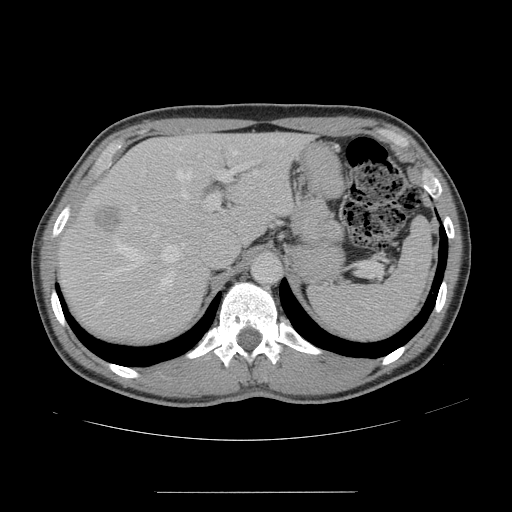
Contrast-enhanced abdominal CT, one axial slice. Slice 107 of 178 in the series (ordered by position). 120 kVp. Intravenous contrast given. Soft-tissue window (W 400 / L 40 HU). 2.5 mm slice thickness. 512 × 512 image matrix, field of view 401 × 401 mm. Male patient, age 53 years. From the clinical record (not read from this slice): diagnosis: colorectal cancer liver metastases, imaged before liver resection; multiple liver metastases: yes; largest metastasis: 2.4 cm.
Annotated regions visible in this slice (outlined manually by an expert reader):
- hepatic veins: box from (x=100, y=140) to (x=283, y=303) px
- liver: (x=62, y=134)–(x=304, y=339)
- planned liver remnant (the part of the liver to remain after resection): (x=148, y=135)–(x=304, y=241)
- portal vein (with intrahepatic branches): (x=132, y=155)–(x=256, y=237)
- liver metastasis: (x=95, y=207)–(x=123, y=234)